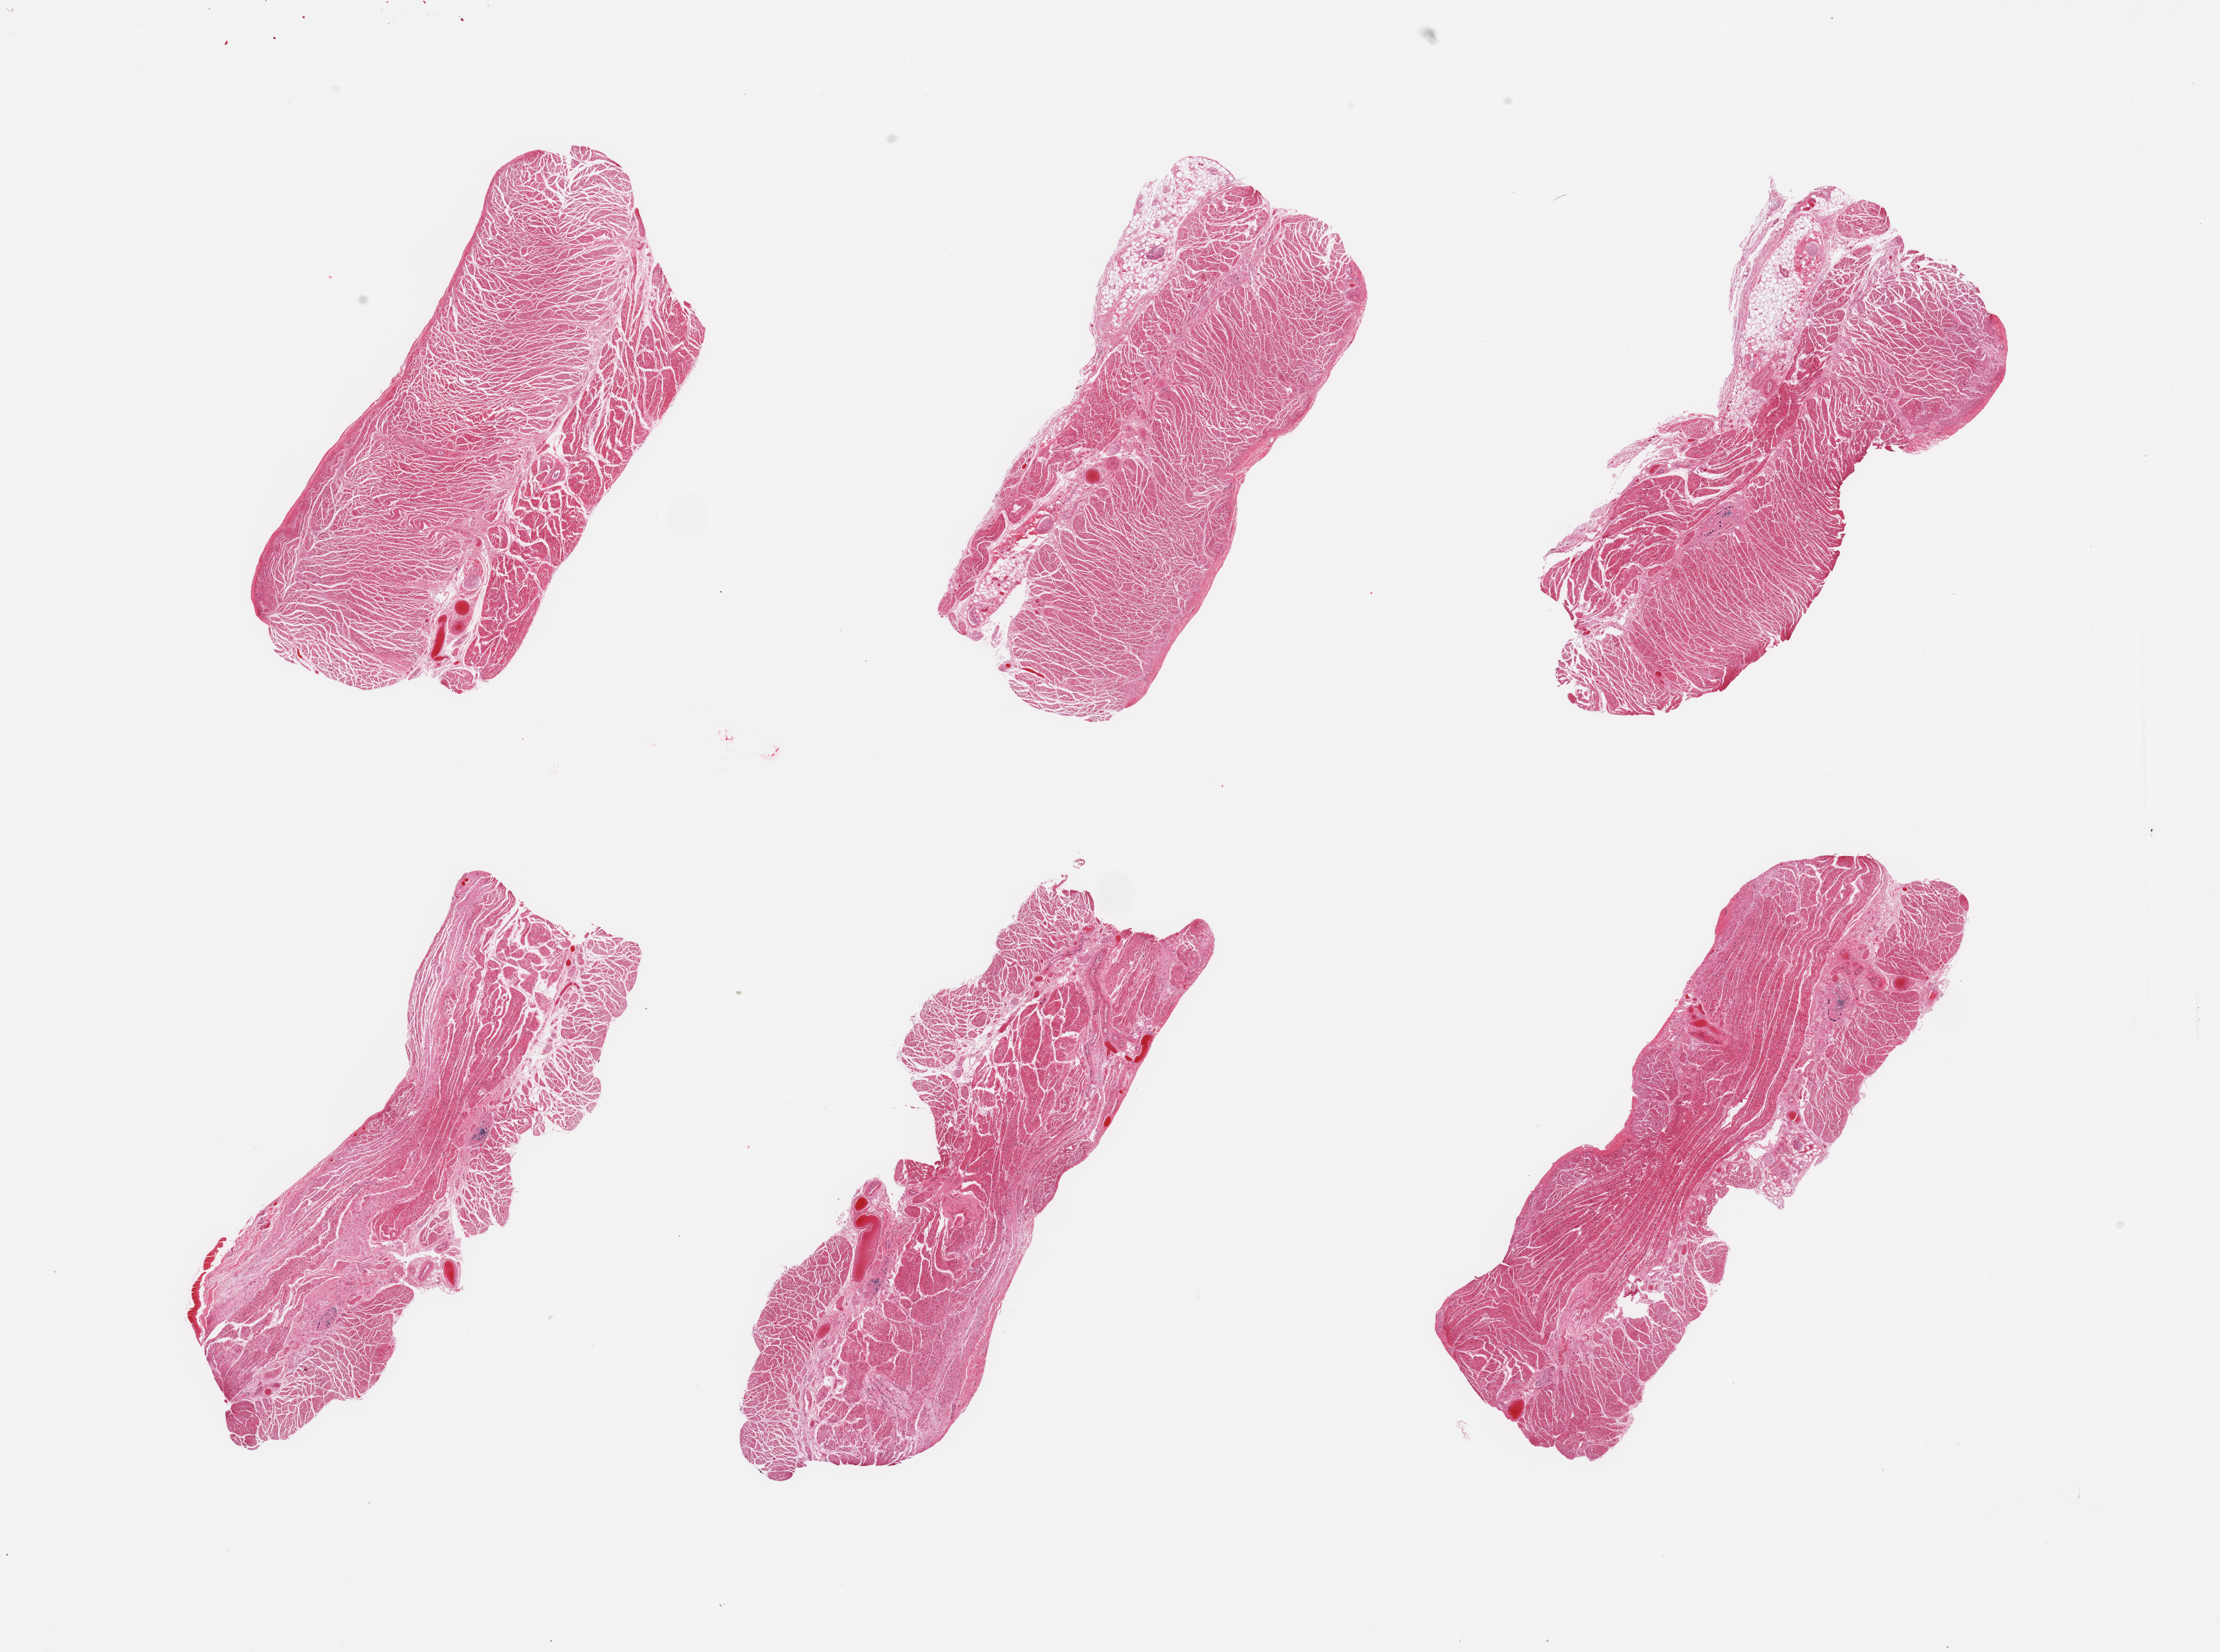
Whole-slide image, hematoxylin and eosin (H&E) stain, brightfield — shown as a low-resolution overview of the whole scanned area (about 26.6 x 19.8 mm, slide scanned at 20x), PAXgene-fixed paraffin-embedded (PFPE) section, sampled site (target tissue): gastroesophageal junction, donor tissue sample. Donor sex: male.
Review note (as recorded): 6 pieces.